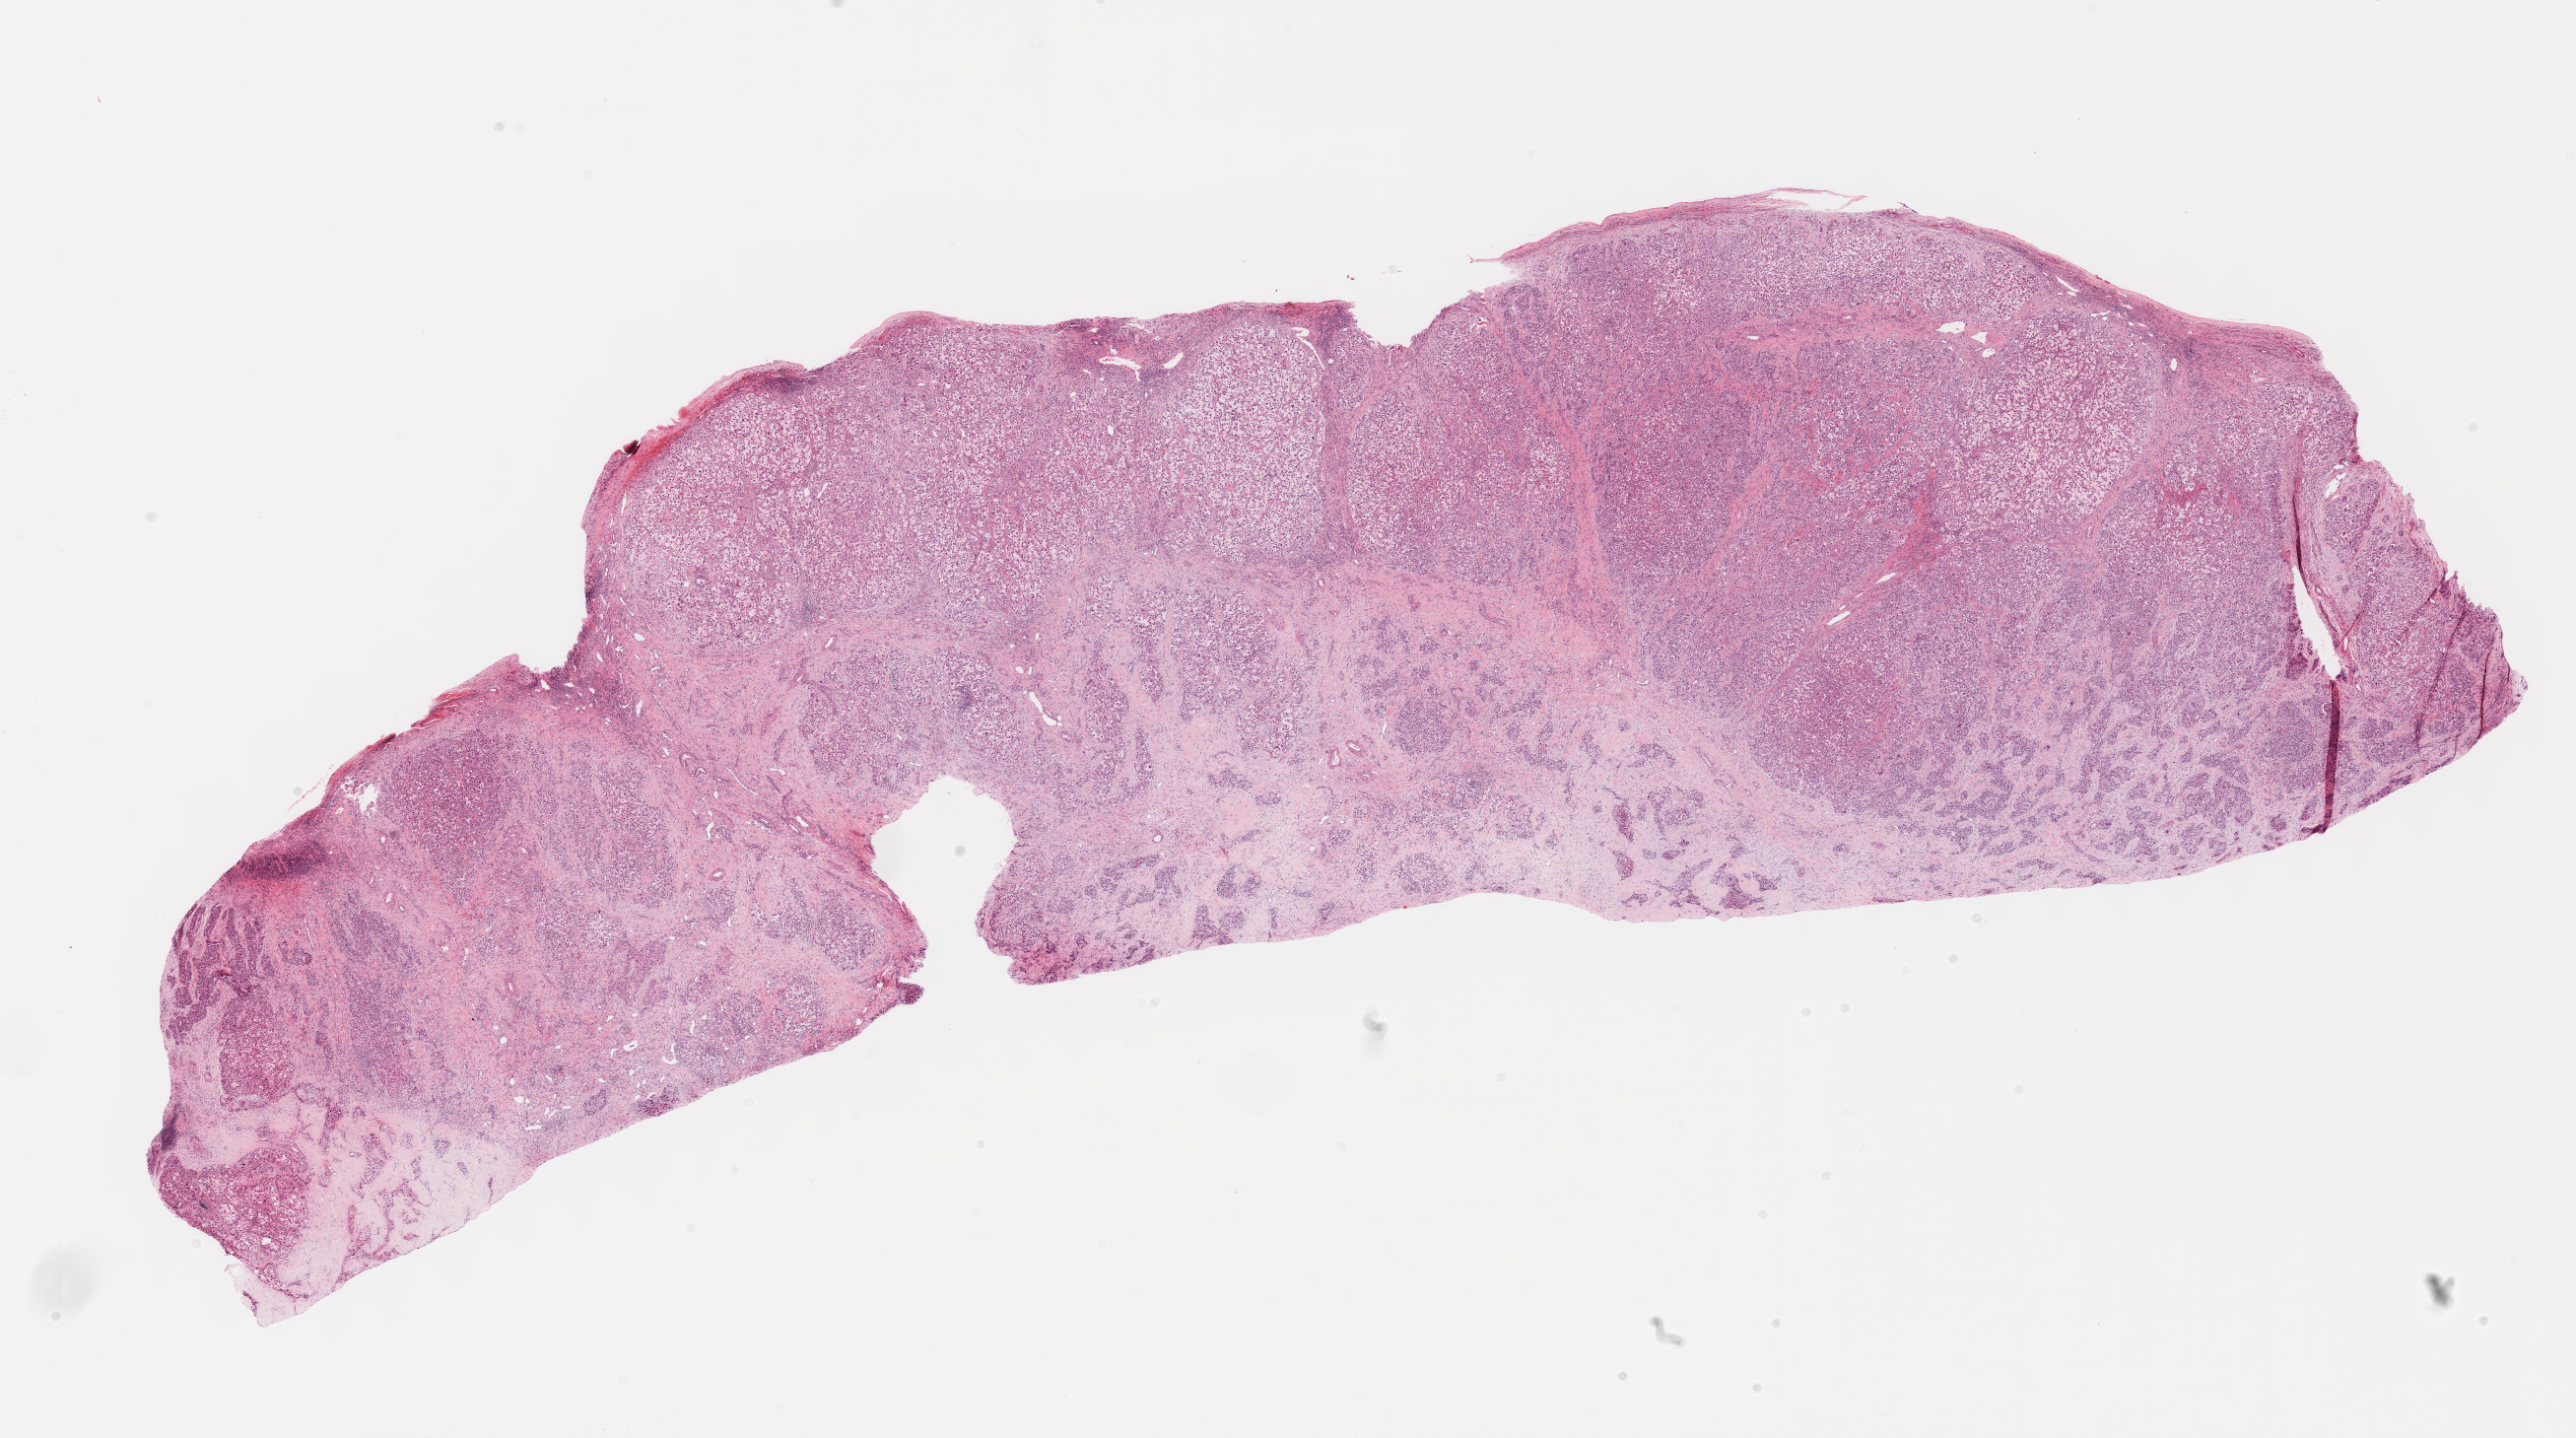
H&E-stained whole-slide image — whole scanned area (about 21.1 x 11.8 mm) shown as a low-resolution overview; FFPE section; primary tumour sample from the liver. Patient: female, age at initial diagnosis 51 years. Histologic grade: G4 (undifferentiated).
Diagnosis: Hepatocellular carcinoma, NOS. AJCC pathologic stage: I (7th edition).